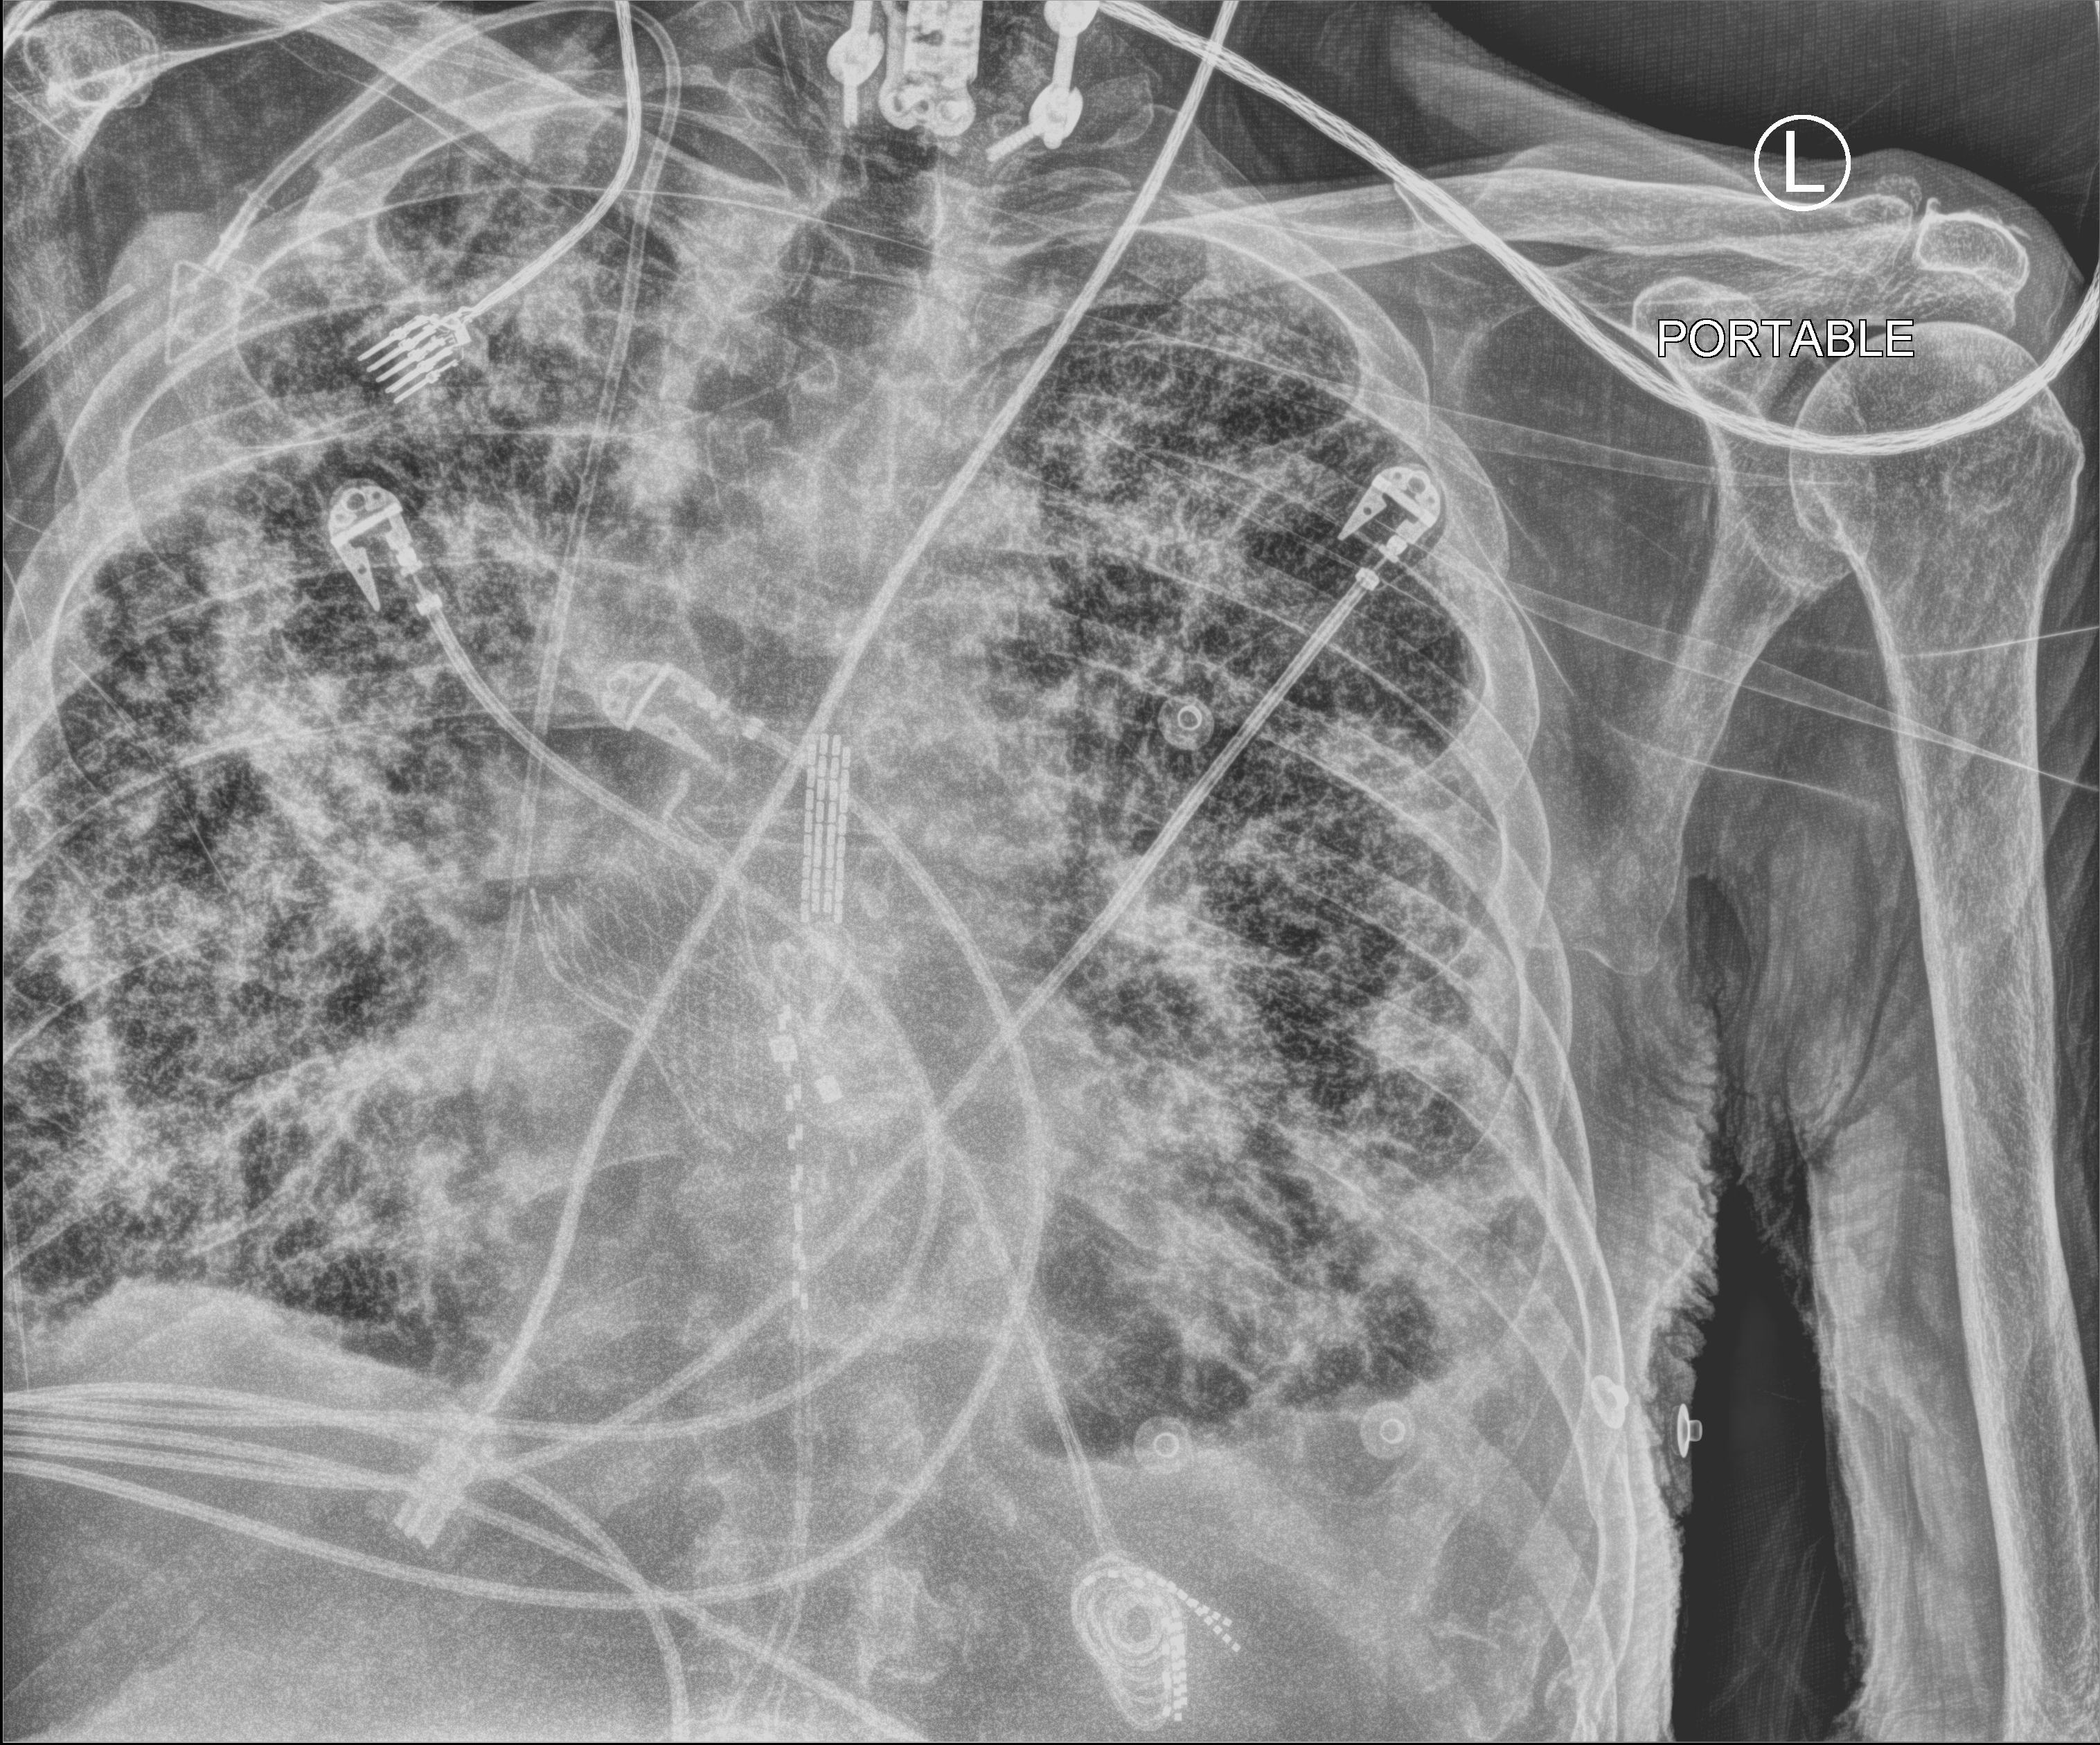
Chest X-ray (portable), anteroposterior (AP) projection. Male patient hospitalised with COVID-19, age 75–90 years.
Hospital-stay facts (about this admission, not read from this image; timing relative to this image not recorded):
- diabetes (admission record): no